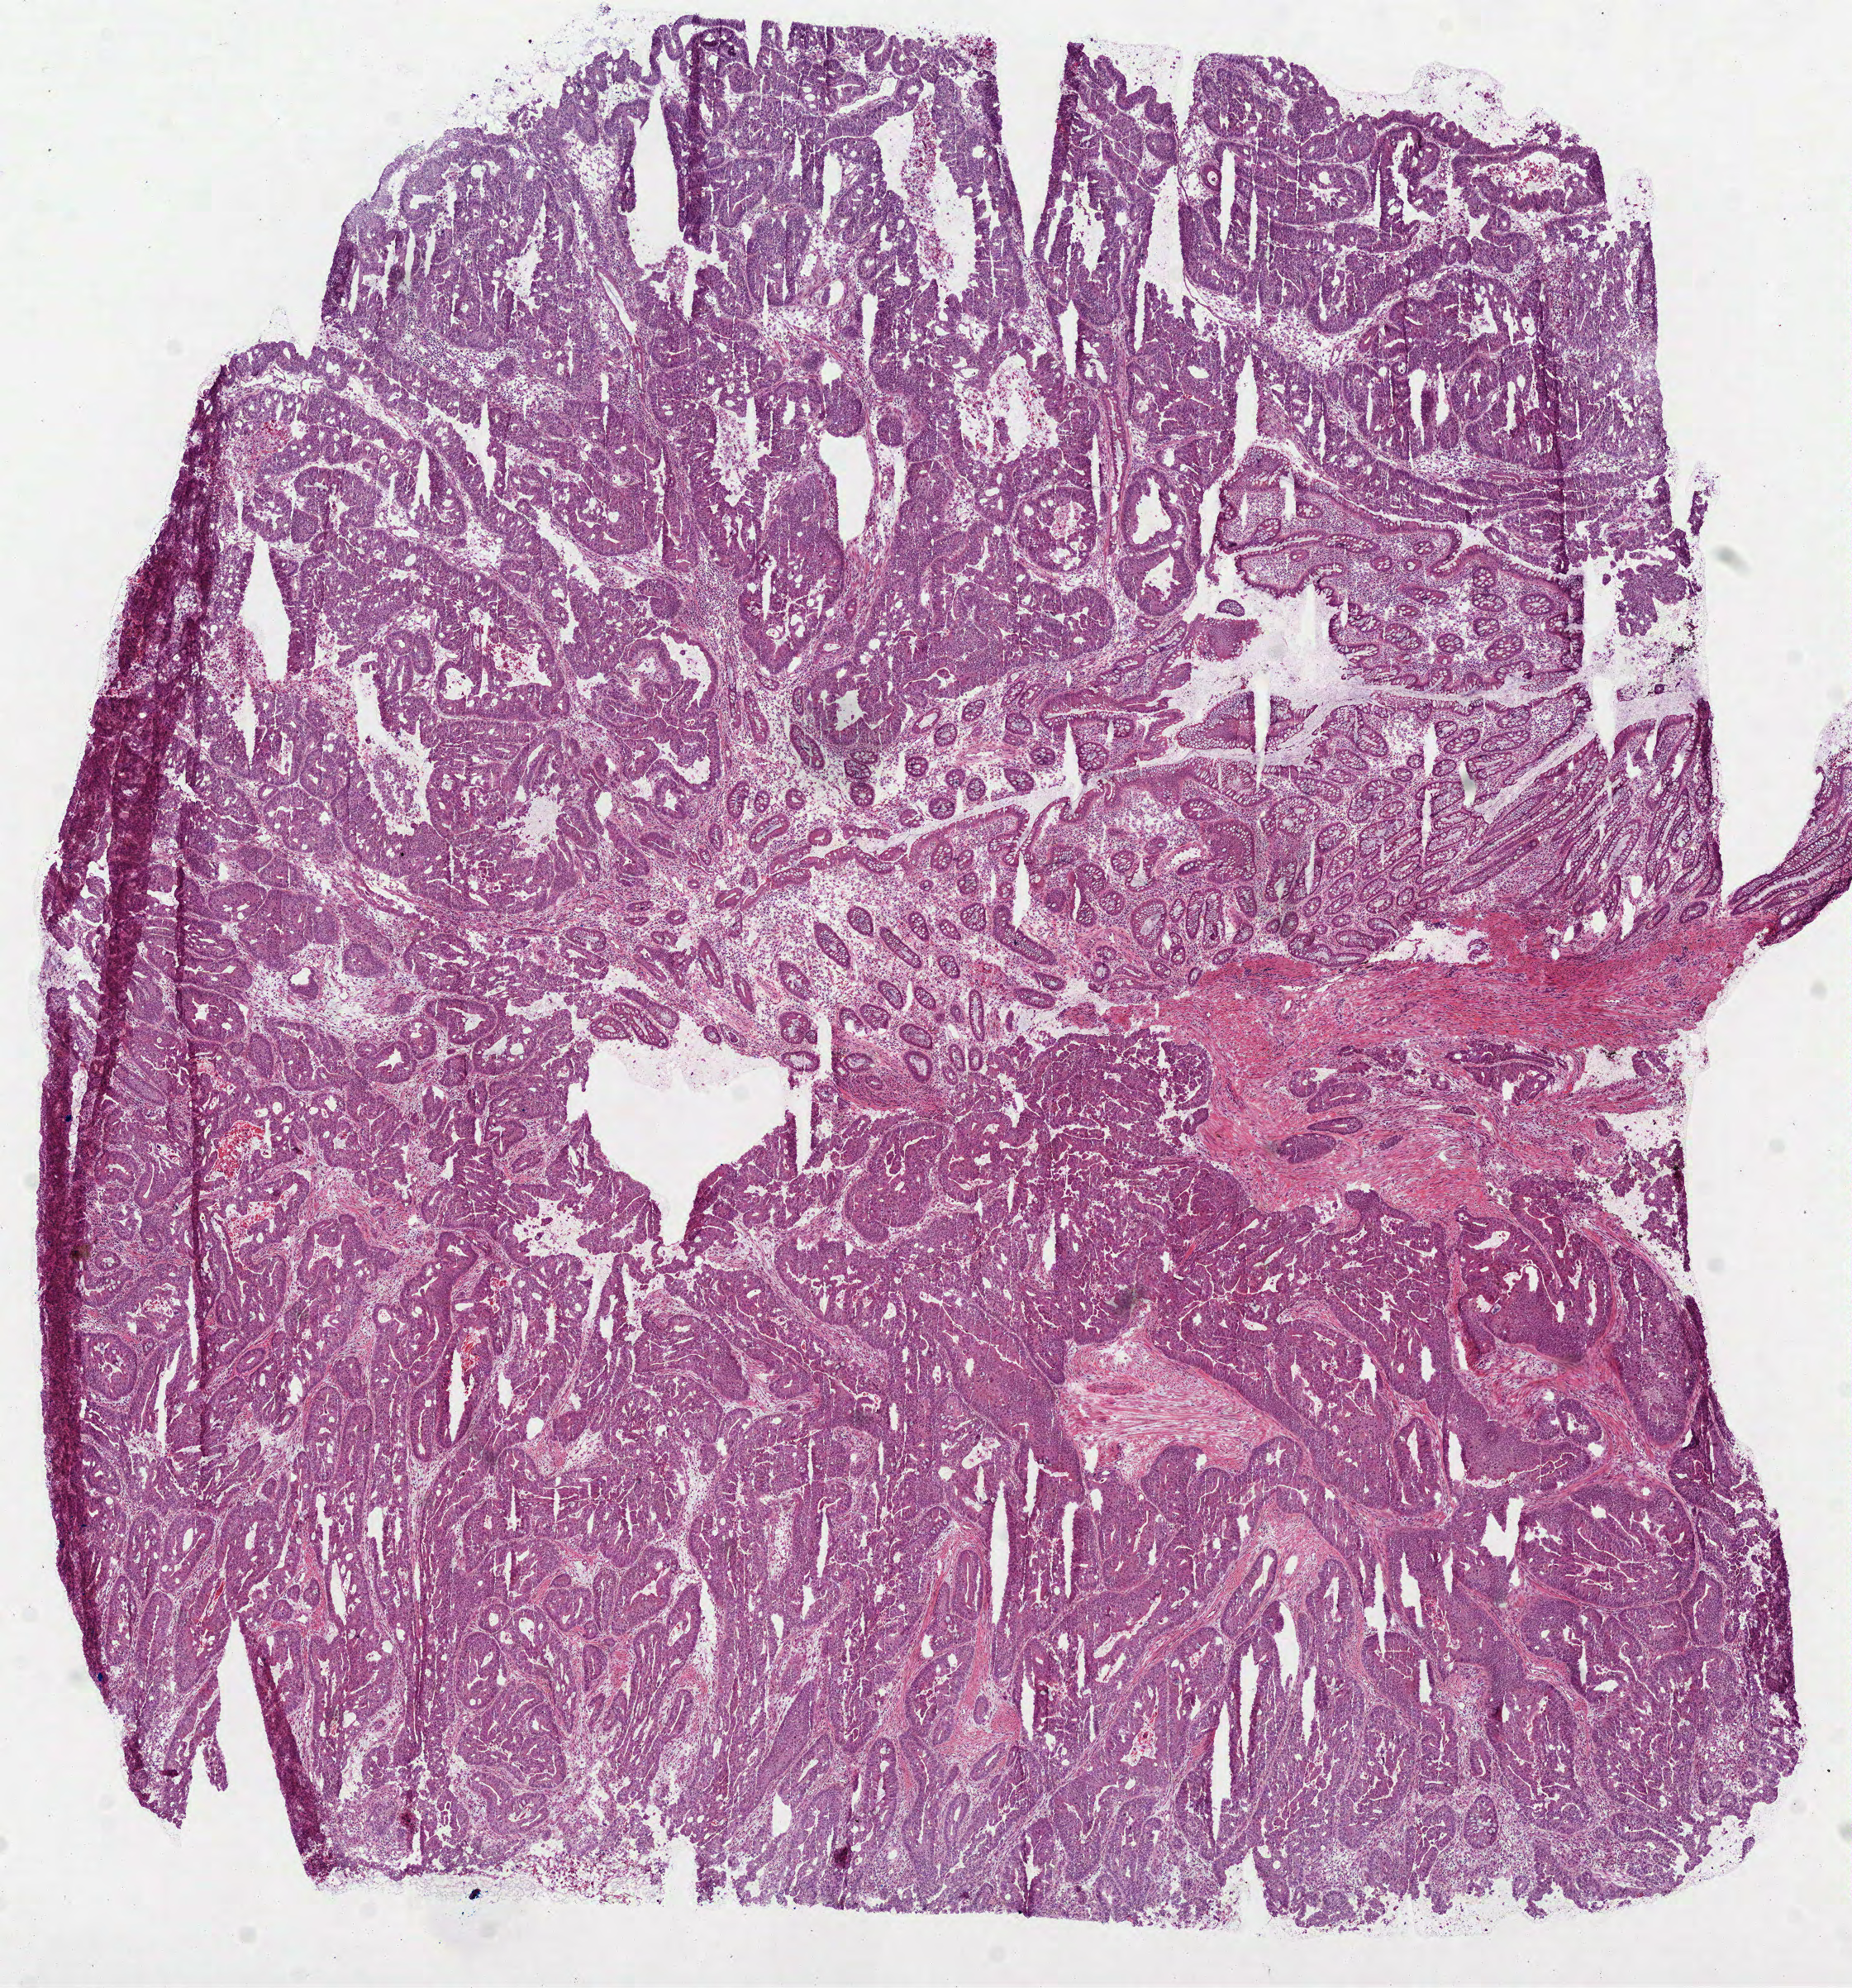
Digitized H&E-stained tissue section (whole slide), a low-resolution overview of the entire scanned area, about 9.0 x 9.7 mm; frozen section from the top of the tissue portion; primary tumour sample from the colon. Patient: female, age at initial diagnosis 69 years. Slide review estimates, as recorded: tumour cells 83%, tumour nuclei 75%, normal cells 15%, stromal cells 0%, necrosis 2%. Inflammatory infiltration, as recorded: lymphocyte infiltration 10%, monocyte infiltration 2%, neutrophil infiltration 5%.
TNM: T3 N0 M0. AJCC pathologic stage: IIA. Diagnosis: Adenocarcinoma, NOS.